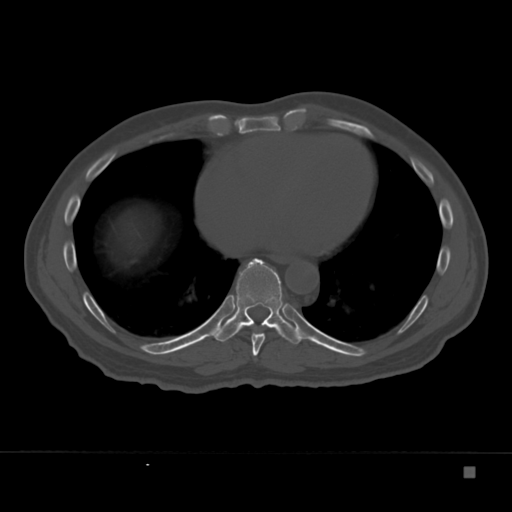
CT including the spine, one axial slice; position 196 of 332 along the scan axis; reconstruction kernel Br40s; bone window (W 1800 / L 400 HU); 512 × 512 image matrix, field of view 389 × 389 mm. Male patient, age 72 years. Case-level facts recorded for this patient, not image findings: primary cancer: skeletal.
Annotated regions visible in this slice (semi-automatically segmented with operator editing):
- T8 vertebra: bounding box [x1, y1, x2, y2] px = [251, 333, 265, 356]
- T9 vertebra: [213, 258, 306, 344]